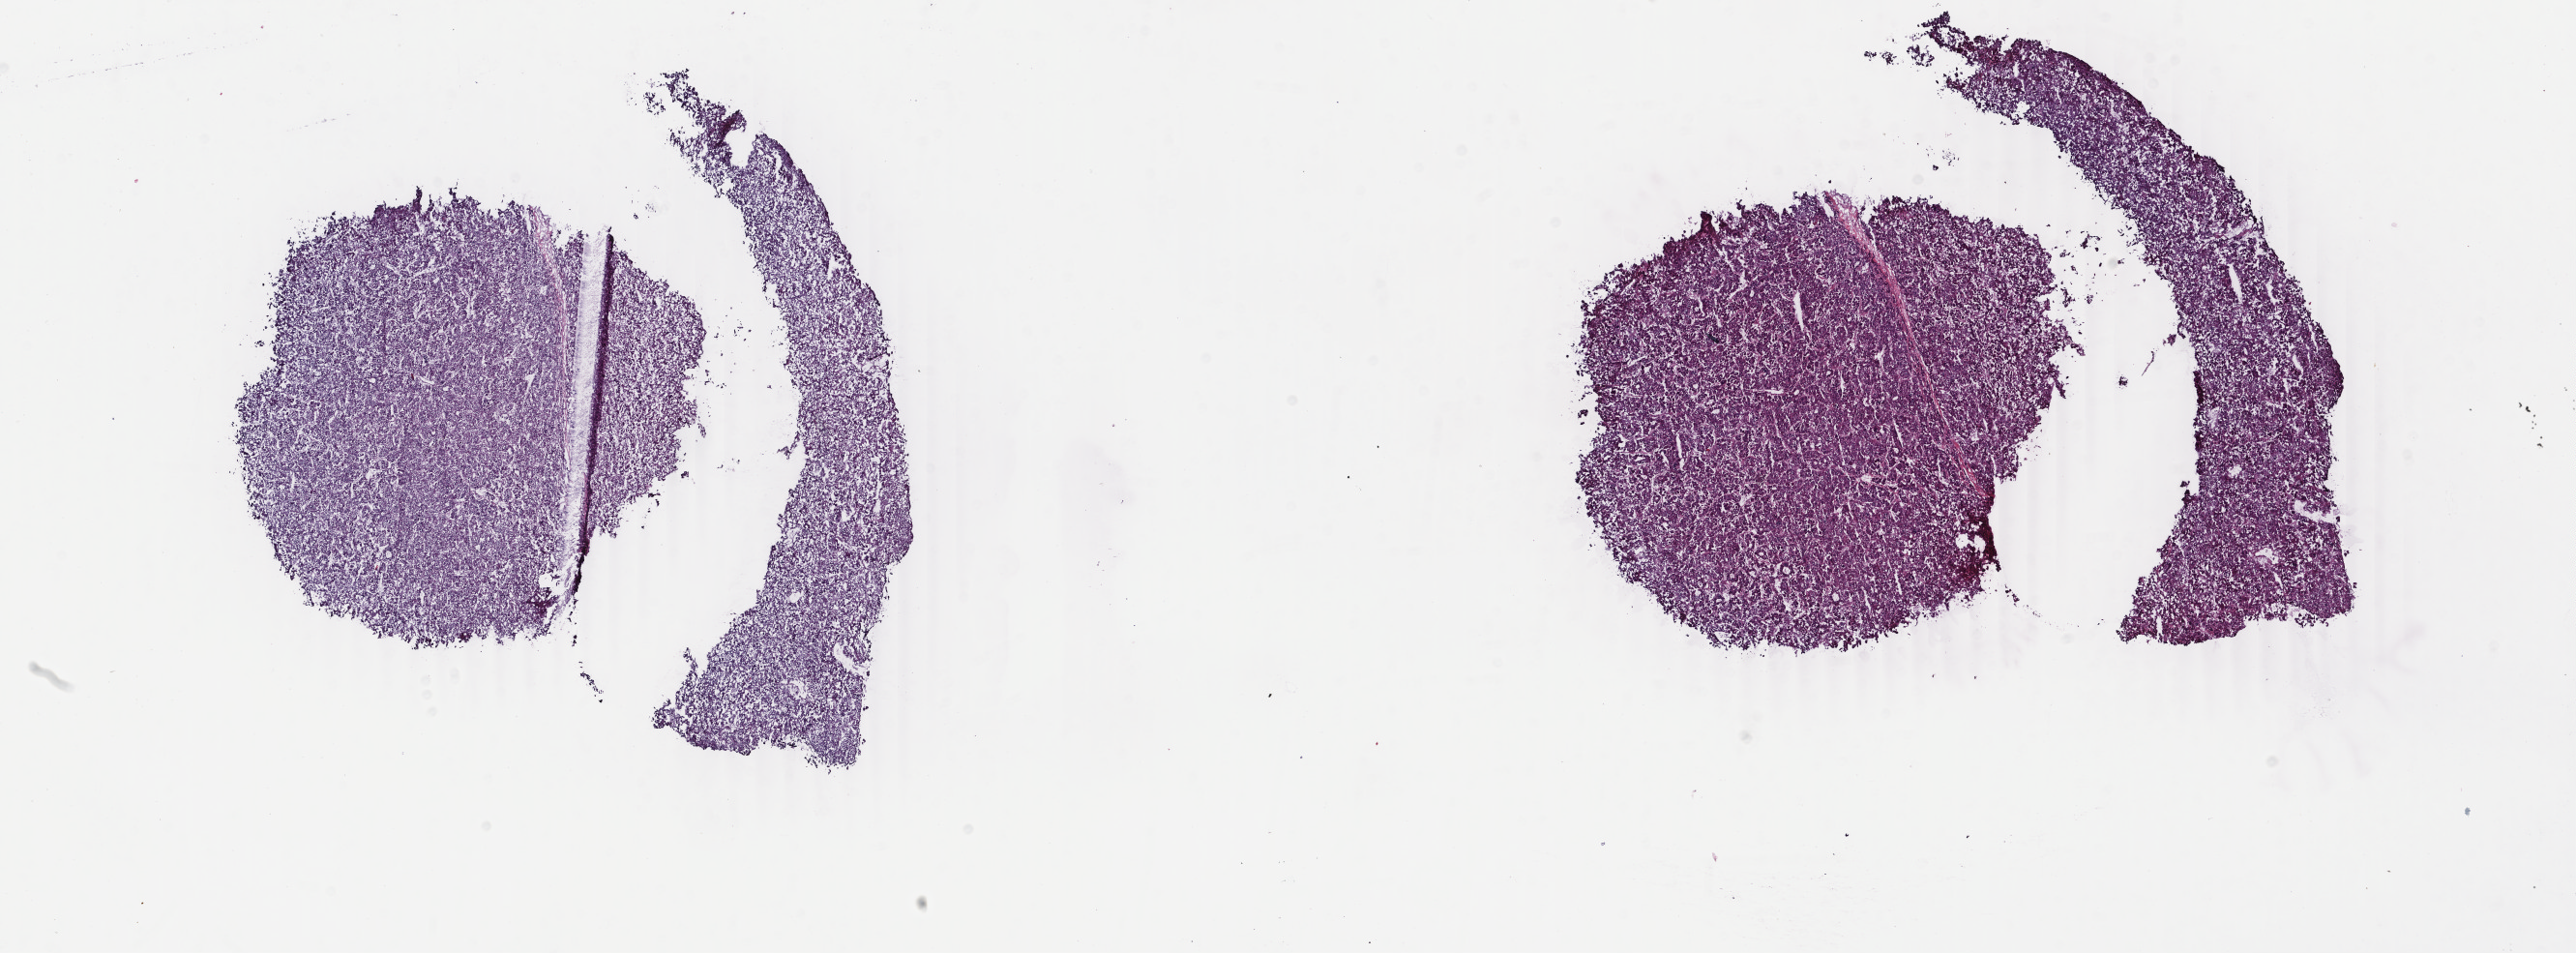
H&E whole-slide image — a low-resolution overview of the entire scanned area, about 21.2 x 7.8 mm; frozen section from the bottom of the tissue portion; primary tumour sample from the liver. Male, age 67 years at initial diagnosis. Histologic grade: G3 (poorly differentiated). Pathologist review of this section (percent, as recorded): tumour cells 85%, tumour nuclei 90%, normal cells 0%, stromal cells 10%, necrosis 5%. Inflammatory infiltration, as recorded: lymphocyte infiltration 2%, monocyte infiltration 0%, neutrophil infiltration 0%.
Histologic diagnosis: Hepatocellular carcinoma, NOS. AJCC pathologic stage: I (6th edition).